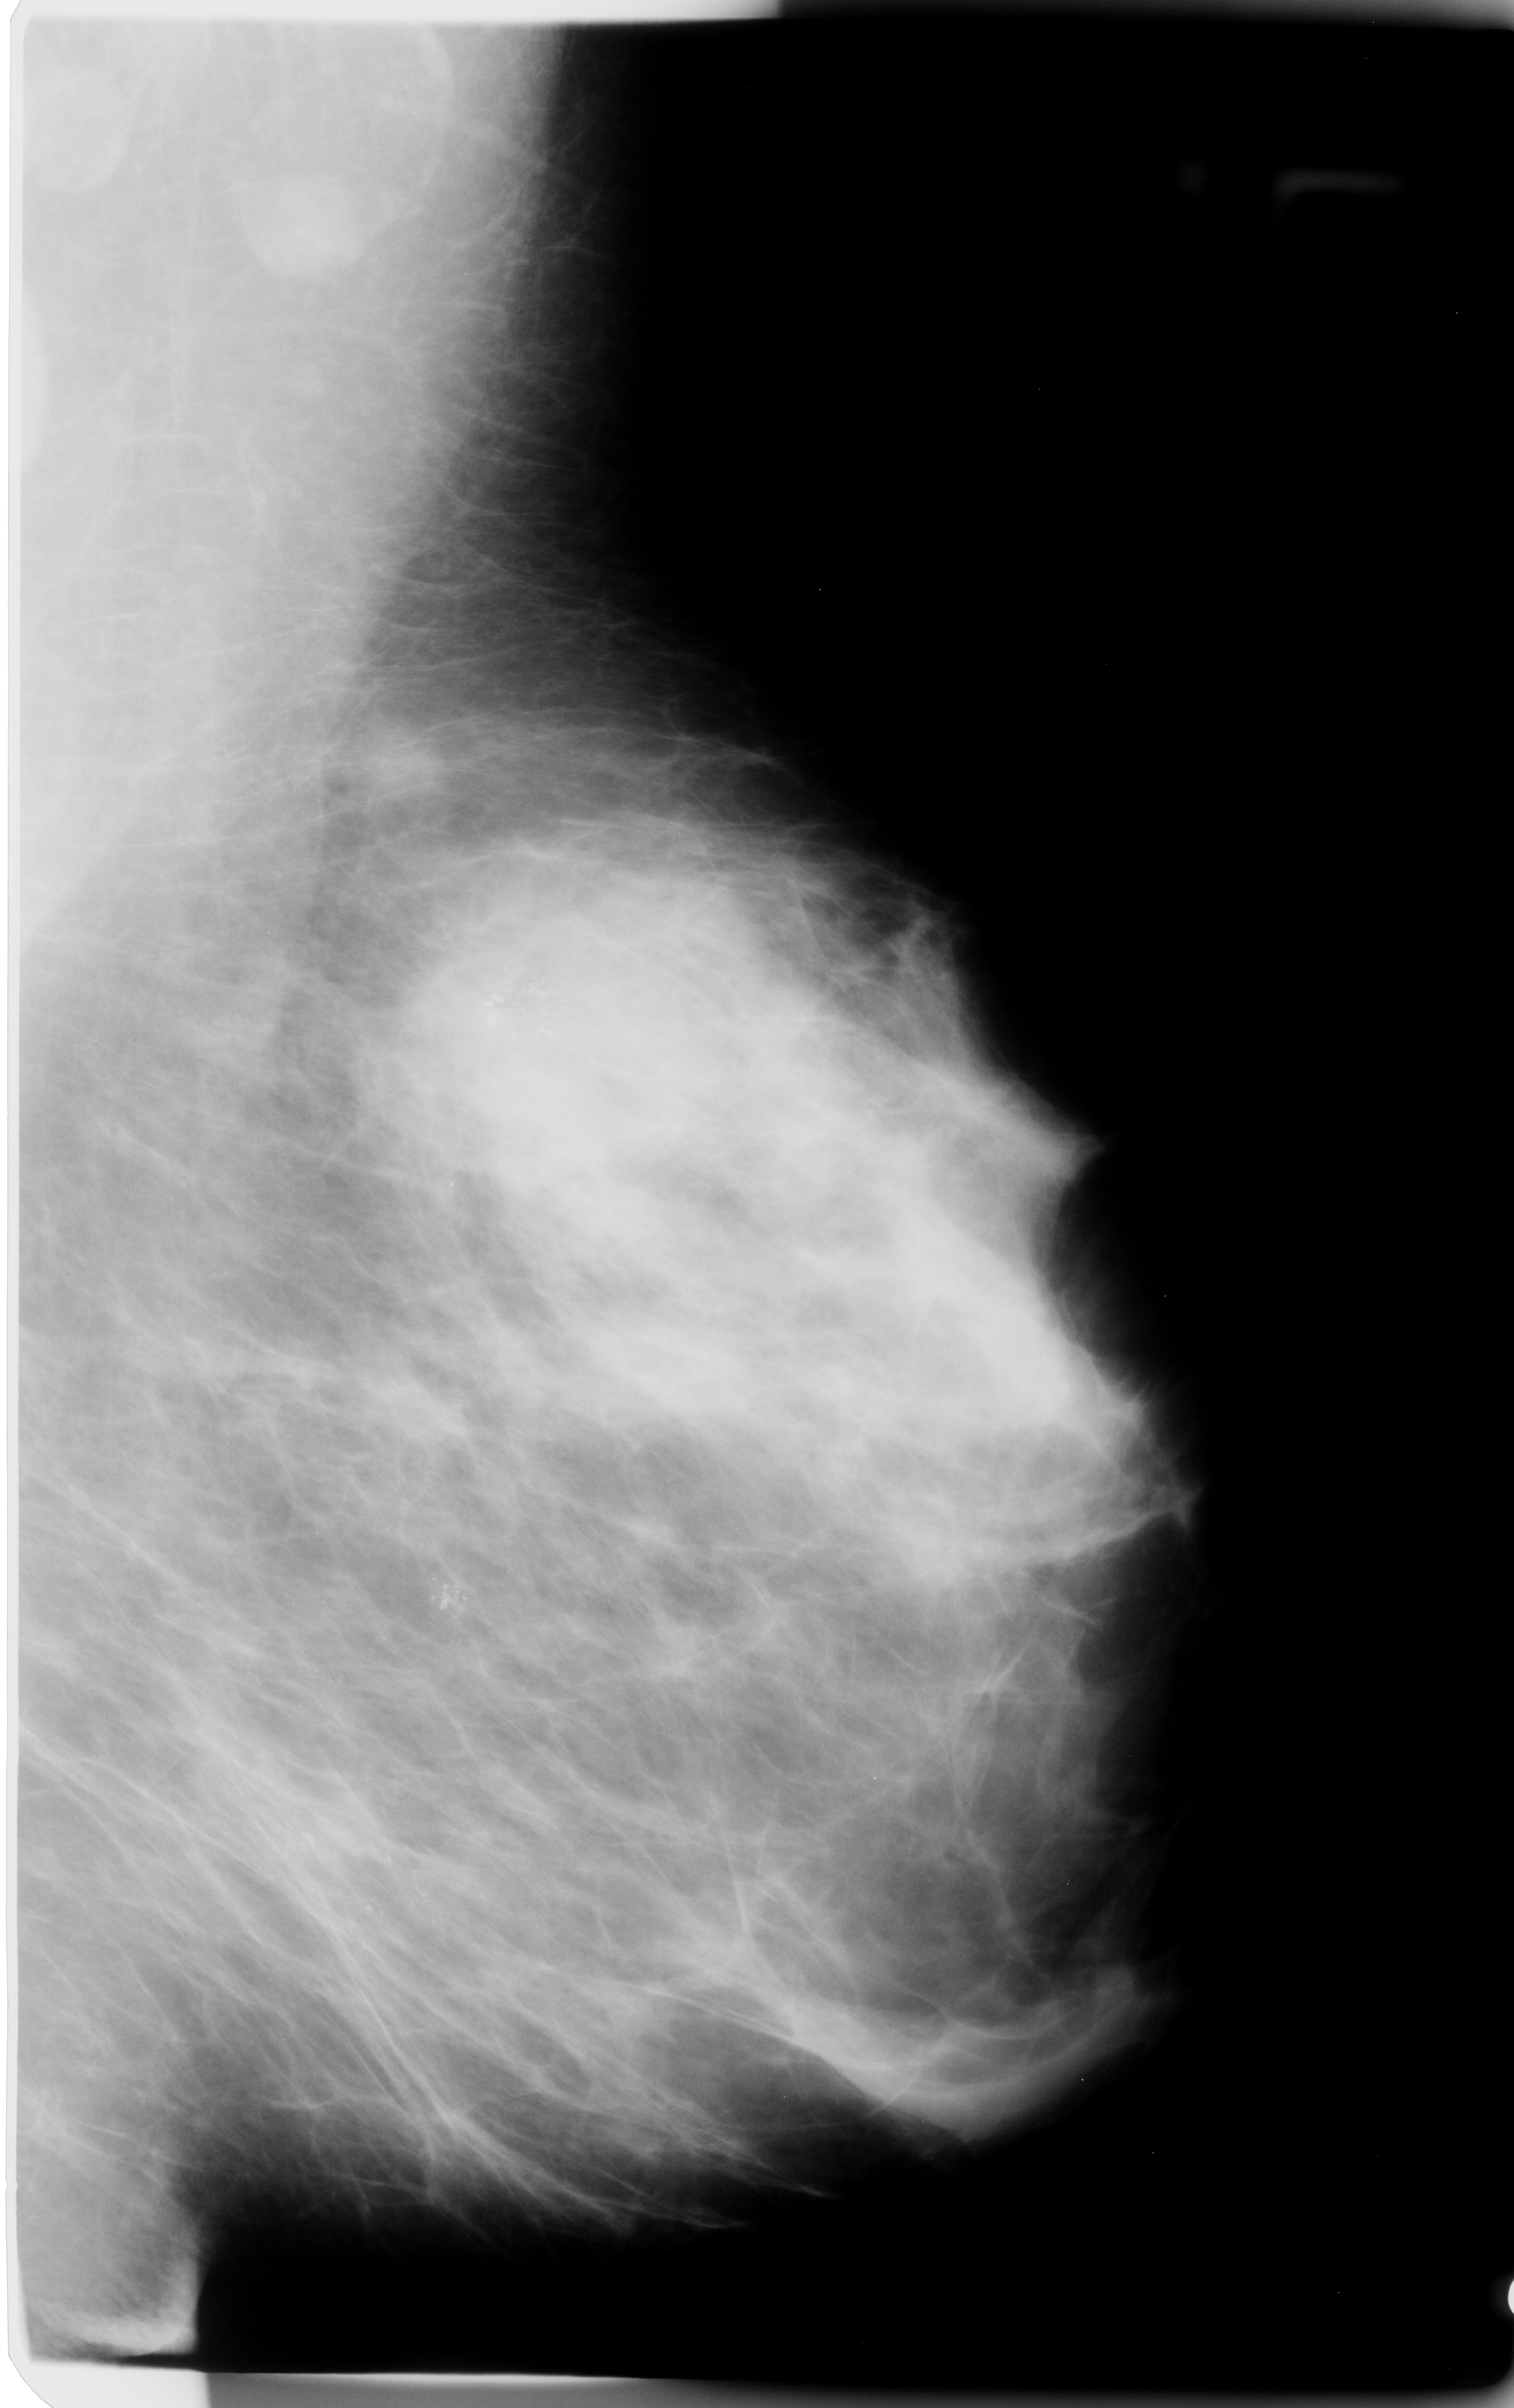
Digitized screen-film mammogram; left breast; mediolateral oblique (MLO) view.
Abnormality record for this image: Finding 1 of 2: calcifications, morphology pleomorphic / fine linear branching, distribution regional; BI-RADS assessment category 5; subtlety rating 3 on a 1 (subtle) to 5 (obvious) scale; pathology (as recorded): malignant. Finding 2 of 2: calcifications, morphology pleomorphic / fine linear branching, distribution regional; BI-RADS assessment category 5; subtlety rating 3 on a 1 (subtle) to 5 (obvious) scale; pathology result (as recorded, not read from the image): malignant.